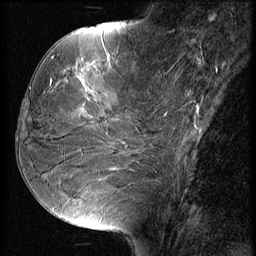
Breast MRI (dynamic contrast-enhanced), one sagittal slice. Position 23 of 56 along the scan axis. 3 images stored at this slice position (order not interpretable as contrast timing). 1.5 T. TE 4.2 ms, TR 9 ms. 2.5 mm slice thickness. 256 × 256 image matrix. Patient: female, 51 years. Case-level facts recorded for this patient, not image findings: setting: breast cancer imaged before/during neoadjuvant chemotherapy; receptor status: HR-positive, HER2-negative.
Annotated regions visible in this slice (semi-automatic segmentation, software-assisted and operator-edited):
- analysis volume of interest (the breast-tissue region the enhancement analysis was run in; not a lesion): bounding box (x1, y1, x2, y2) in pixels: (23, 56, 156, 165)
- tumour enhancement mask (voxels above the 140 % enhancement threshold inside the analysis volume of interest): (76, 56, 111, 119)